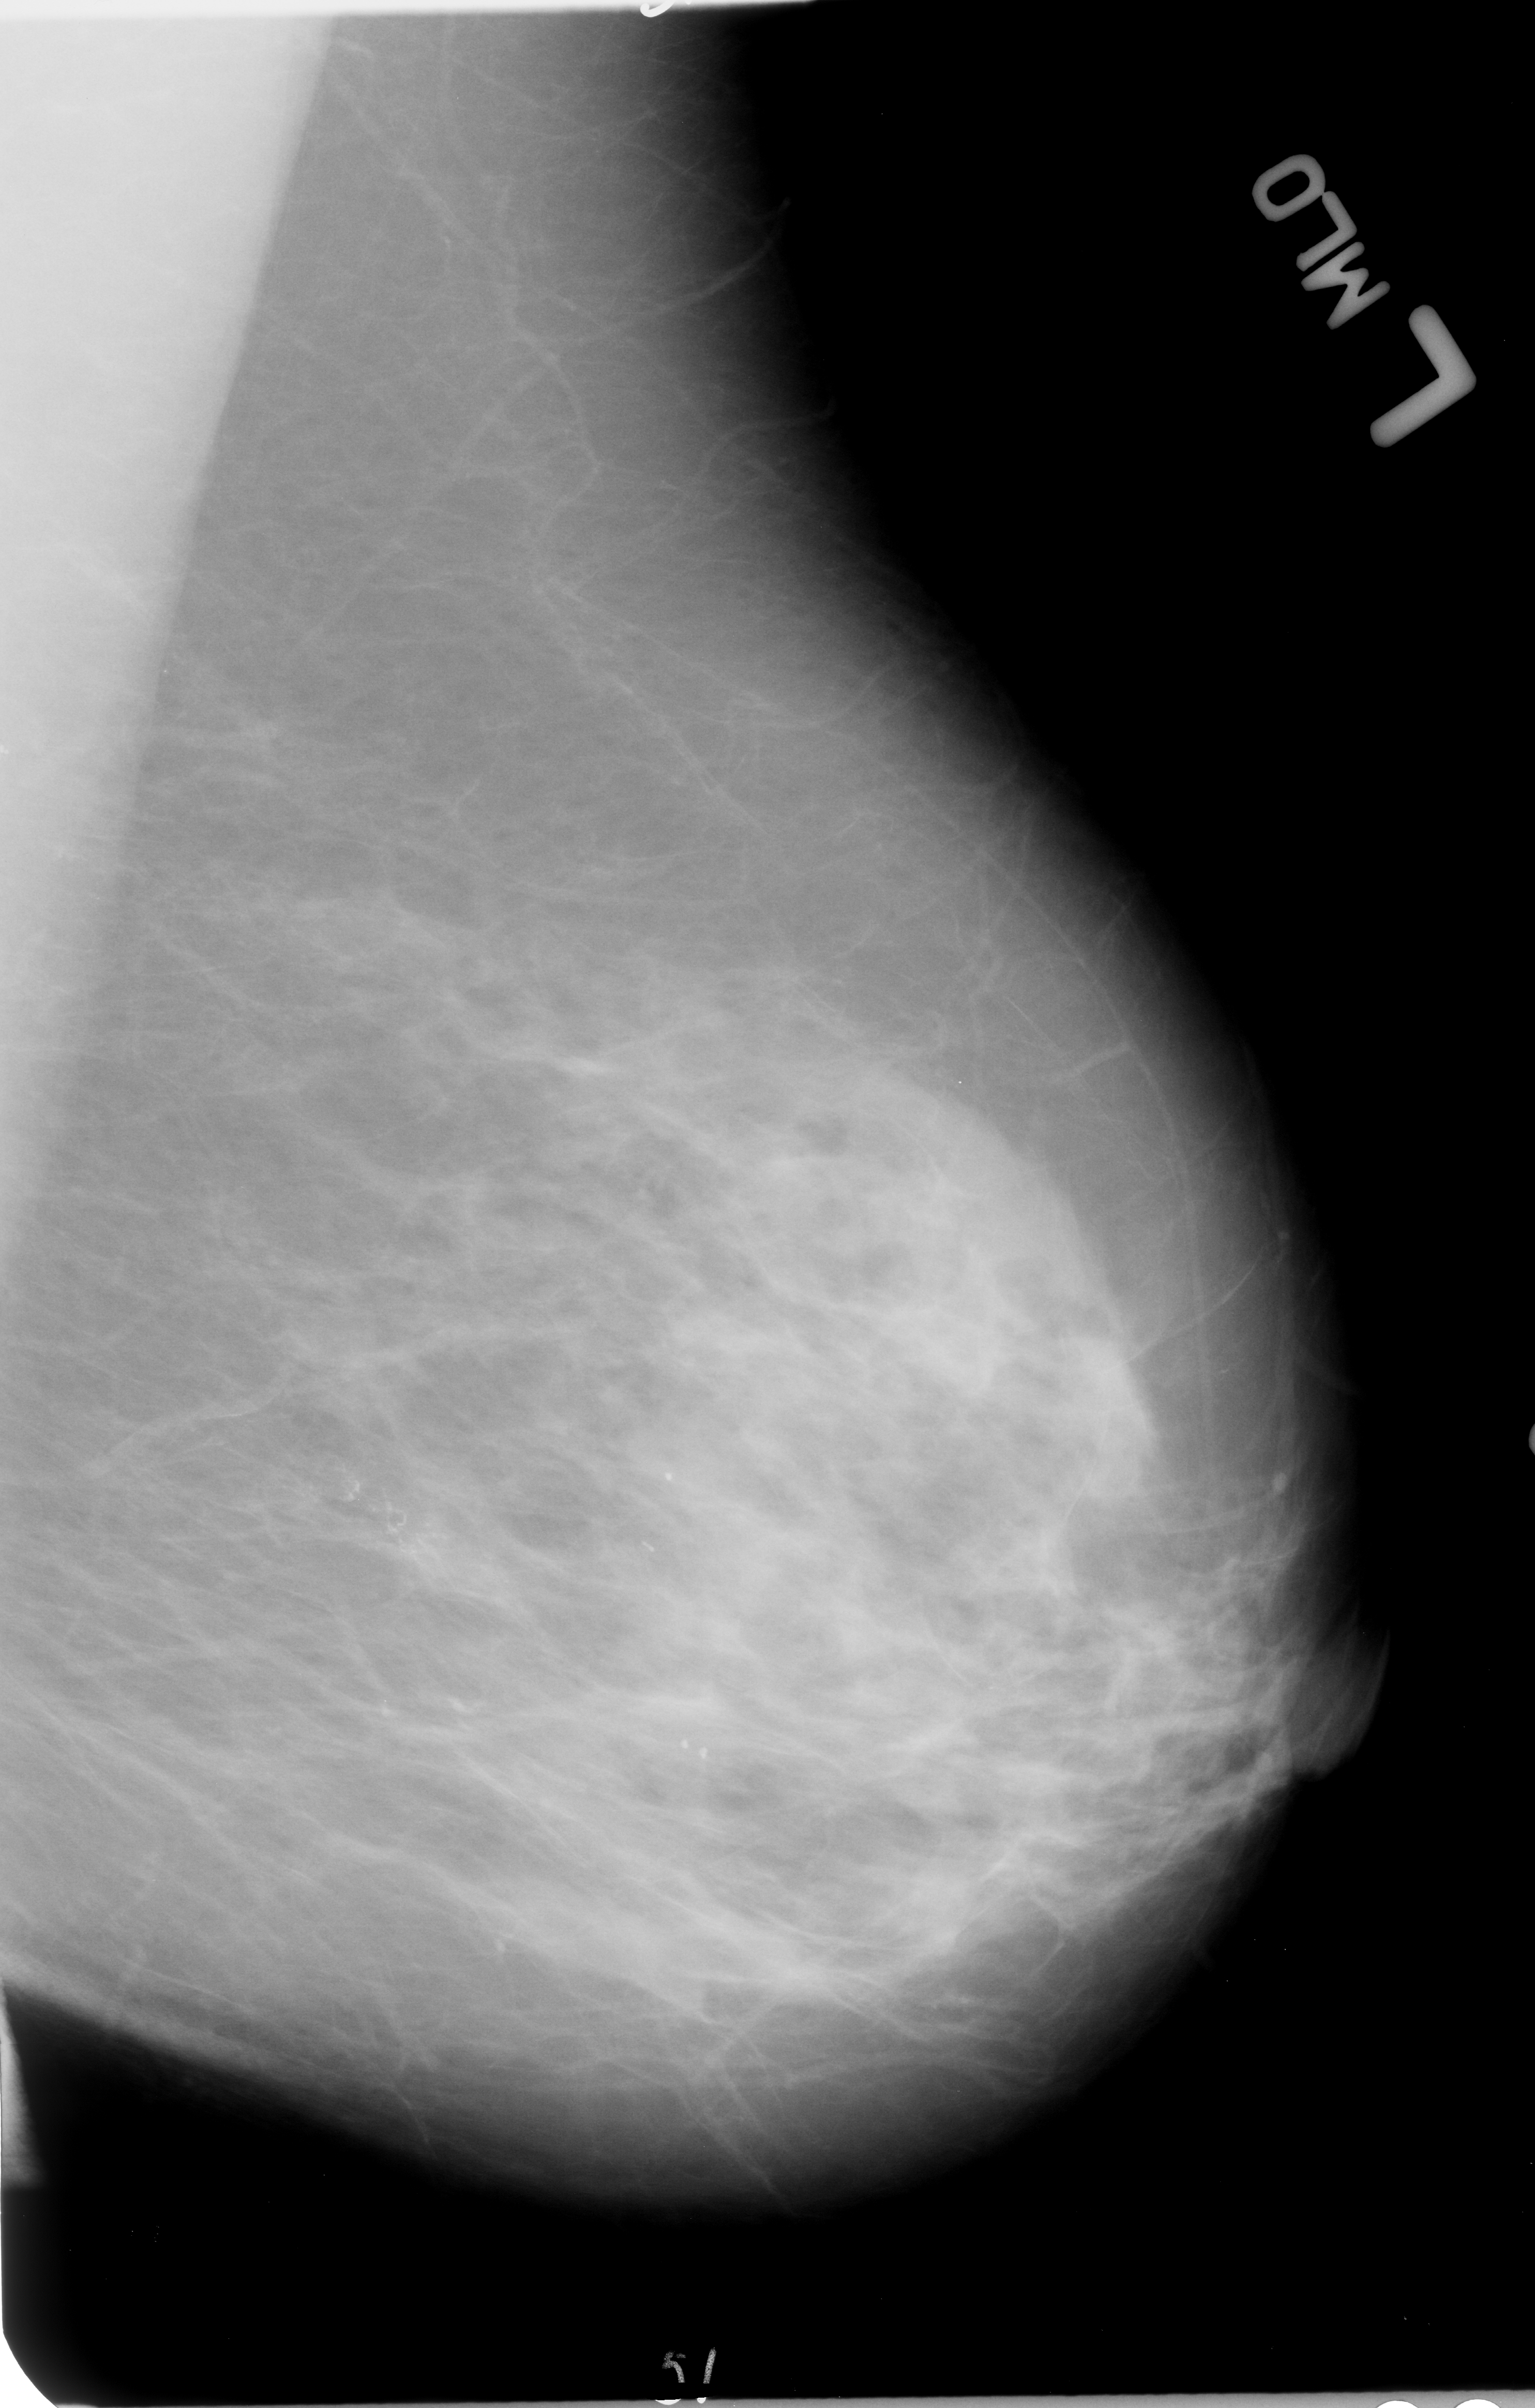
Mammogram (digitized film); left breast; MLO view; BI-RADS breast density category 3 (scale 1–4).
Radiologist-marked abnormalities on this image: calcifications, morphology pleomorphic / fine linear branching, distribution clustered / linear; BI-RADS assessment category 5; pathology (as recorded): malignant.